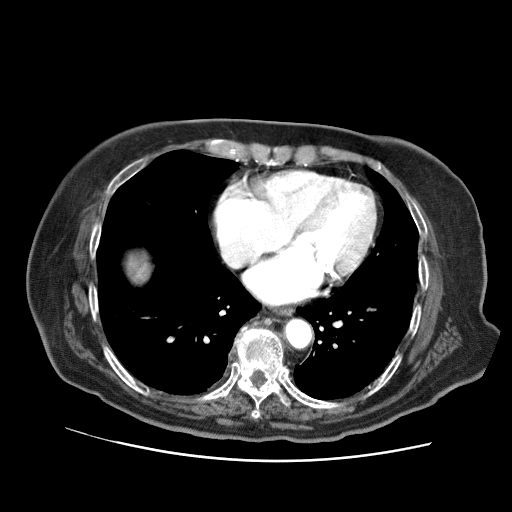
Contrast-enhanced abdominal CT (liver protocol), one axial slice. Slice 67 of 73 in the series (ordered by position). Reconstruction kernel STANDARD. Soft-tissue window (W 400 / L 40 HU). 512 × 512 image matrix, field of view 380 × 380 mm. Case-level facts recorded for this patient, not image findings: diagnosis: hepatocellular carcinoma (patient treated with transarterial chemoembolisation; whether this scan precedes or follows treatment is not stated here); TNM stage (as recorded): Stage-I; Child-Pugh class: A; tumour differentiation: well differentiated; tumour nodularity: uninodular.
Annotated regions visible in this slice (semi-automatic segmentation, software-assisted and operator-edited):
- liver parenchyma outside the tumour (the mass and vessels are separate outlines, so this box may not span the whole liver): box from (x=128, y=256) to (x=148, y=280) px